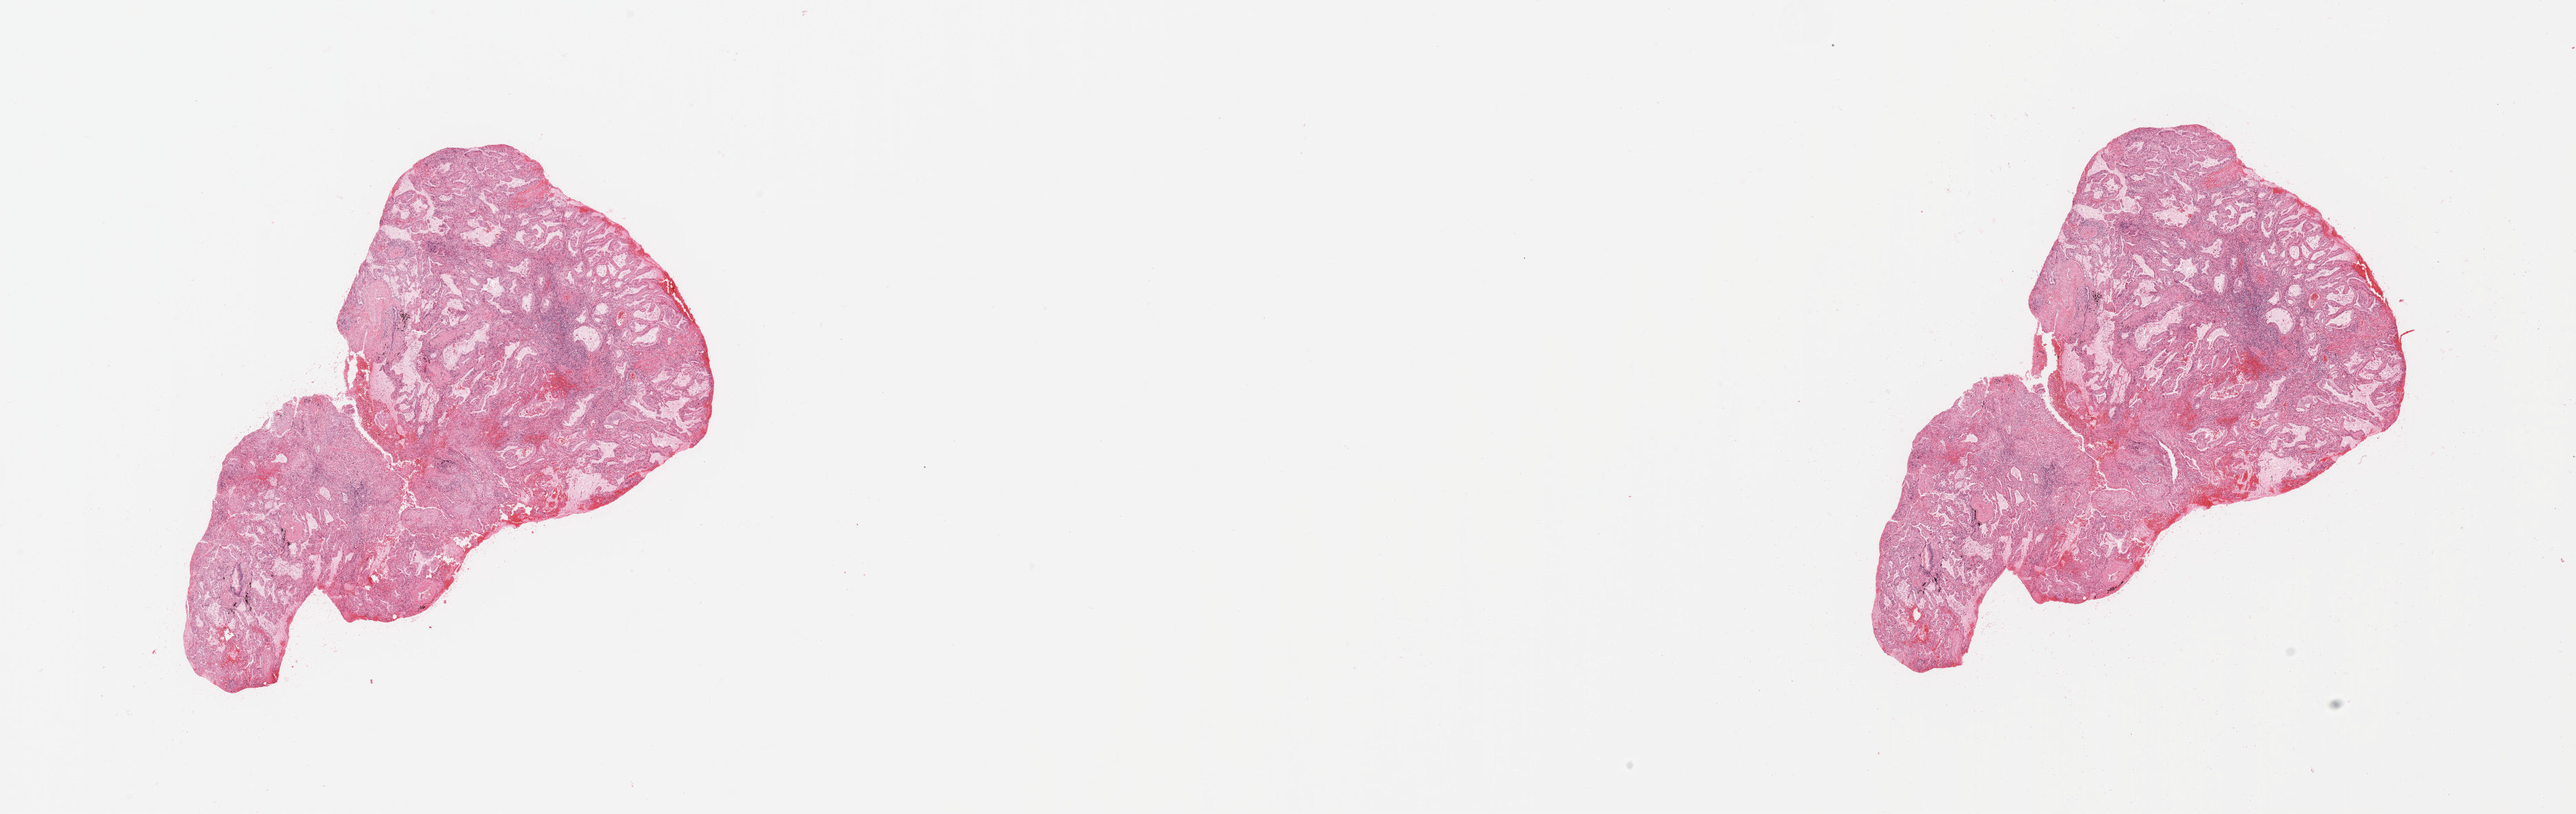
Digitized H&E-stained tissue section (whole slide), shown as a low-resolution overview of the whole scanned area (about 29.5 x 9.3 mm, acquisition: 20x scan), tumour tissue sample, sampled site: lung. Patient: male, age 67 years. Histologic grade: G1 (well differentiated). Slide review estimates, as recorded: tumour nuclei 70%, necrosis 0%.
Histologic diagnosis: Adenocarcinoma, NOS. AJCC pathologic stage: IA.